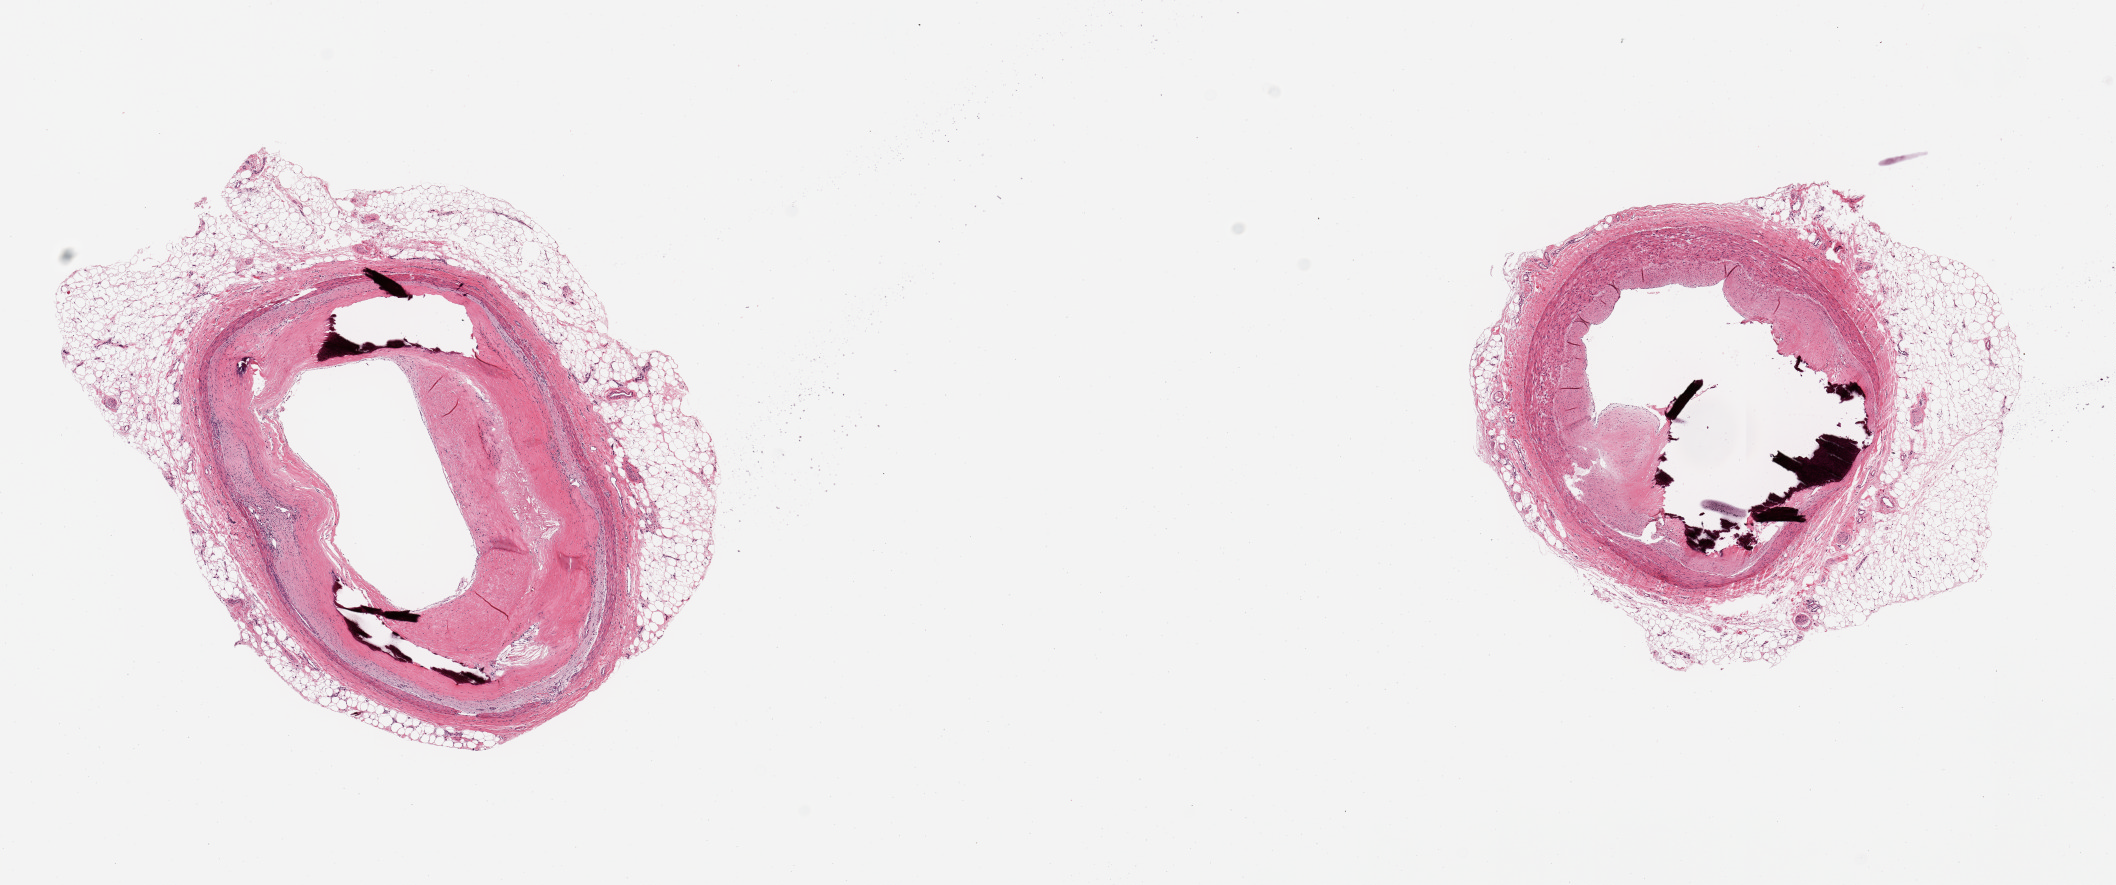
Hematoxylin and eosin (H&E) whole-slide image, brightfield, whole scanned area (about 16.7 x 7.0 mm) shown as a low-resolution overview, PAXgene-fixed paraffin-embedded (PFPE) section, target tissue: coronary artery, donor tissue sample. Donor: female.
Pathologist's review note for this sample: 2 pieces, ~70% occlusive atherosis, focally calcified.